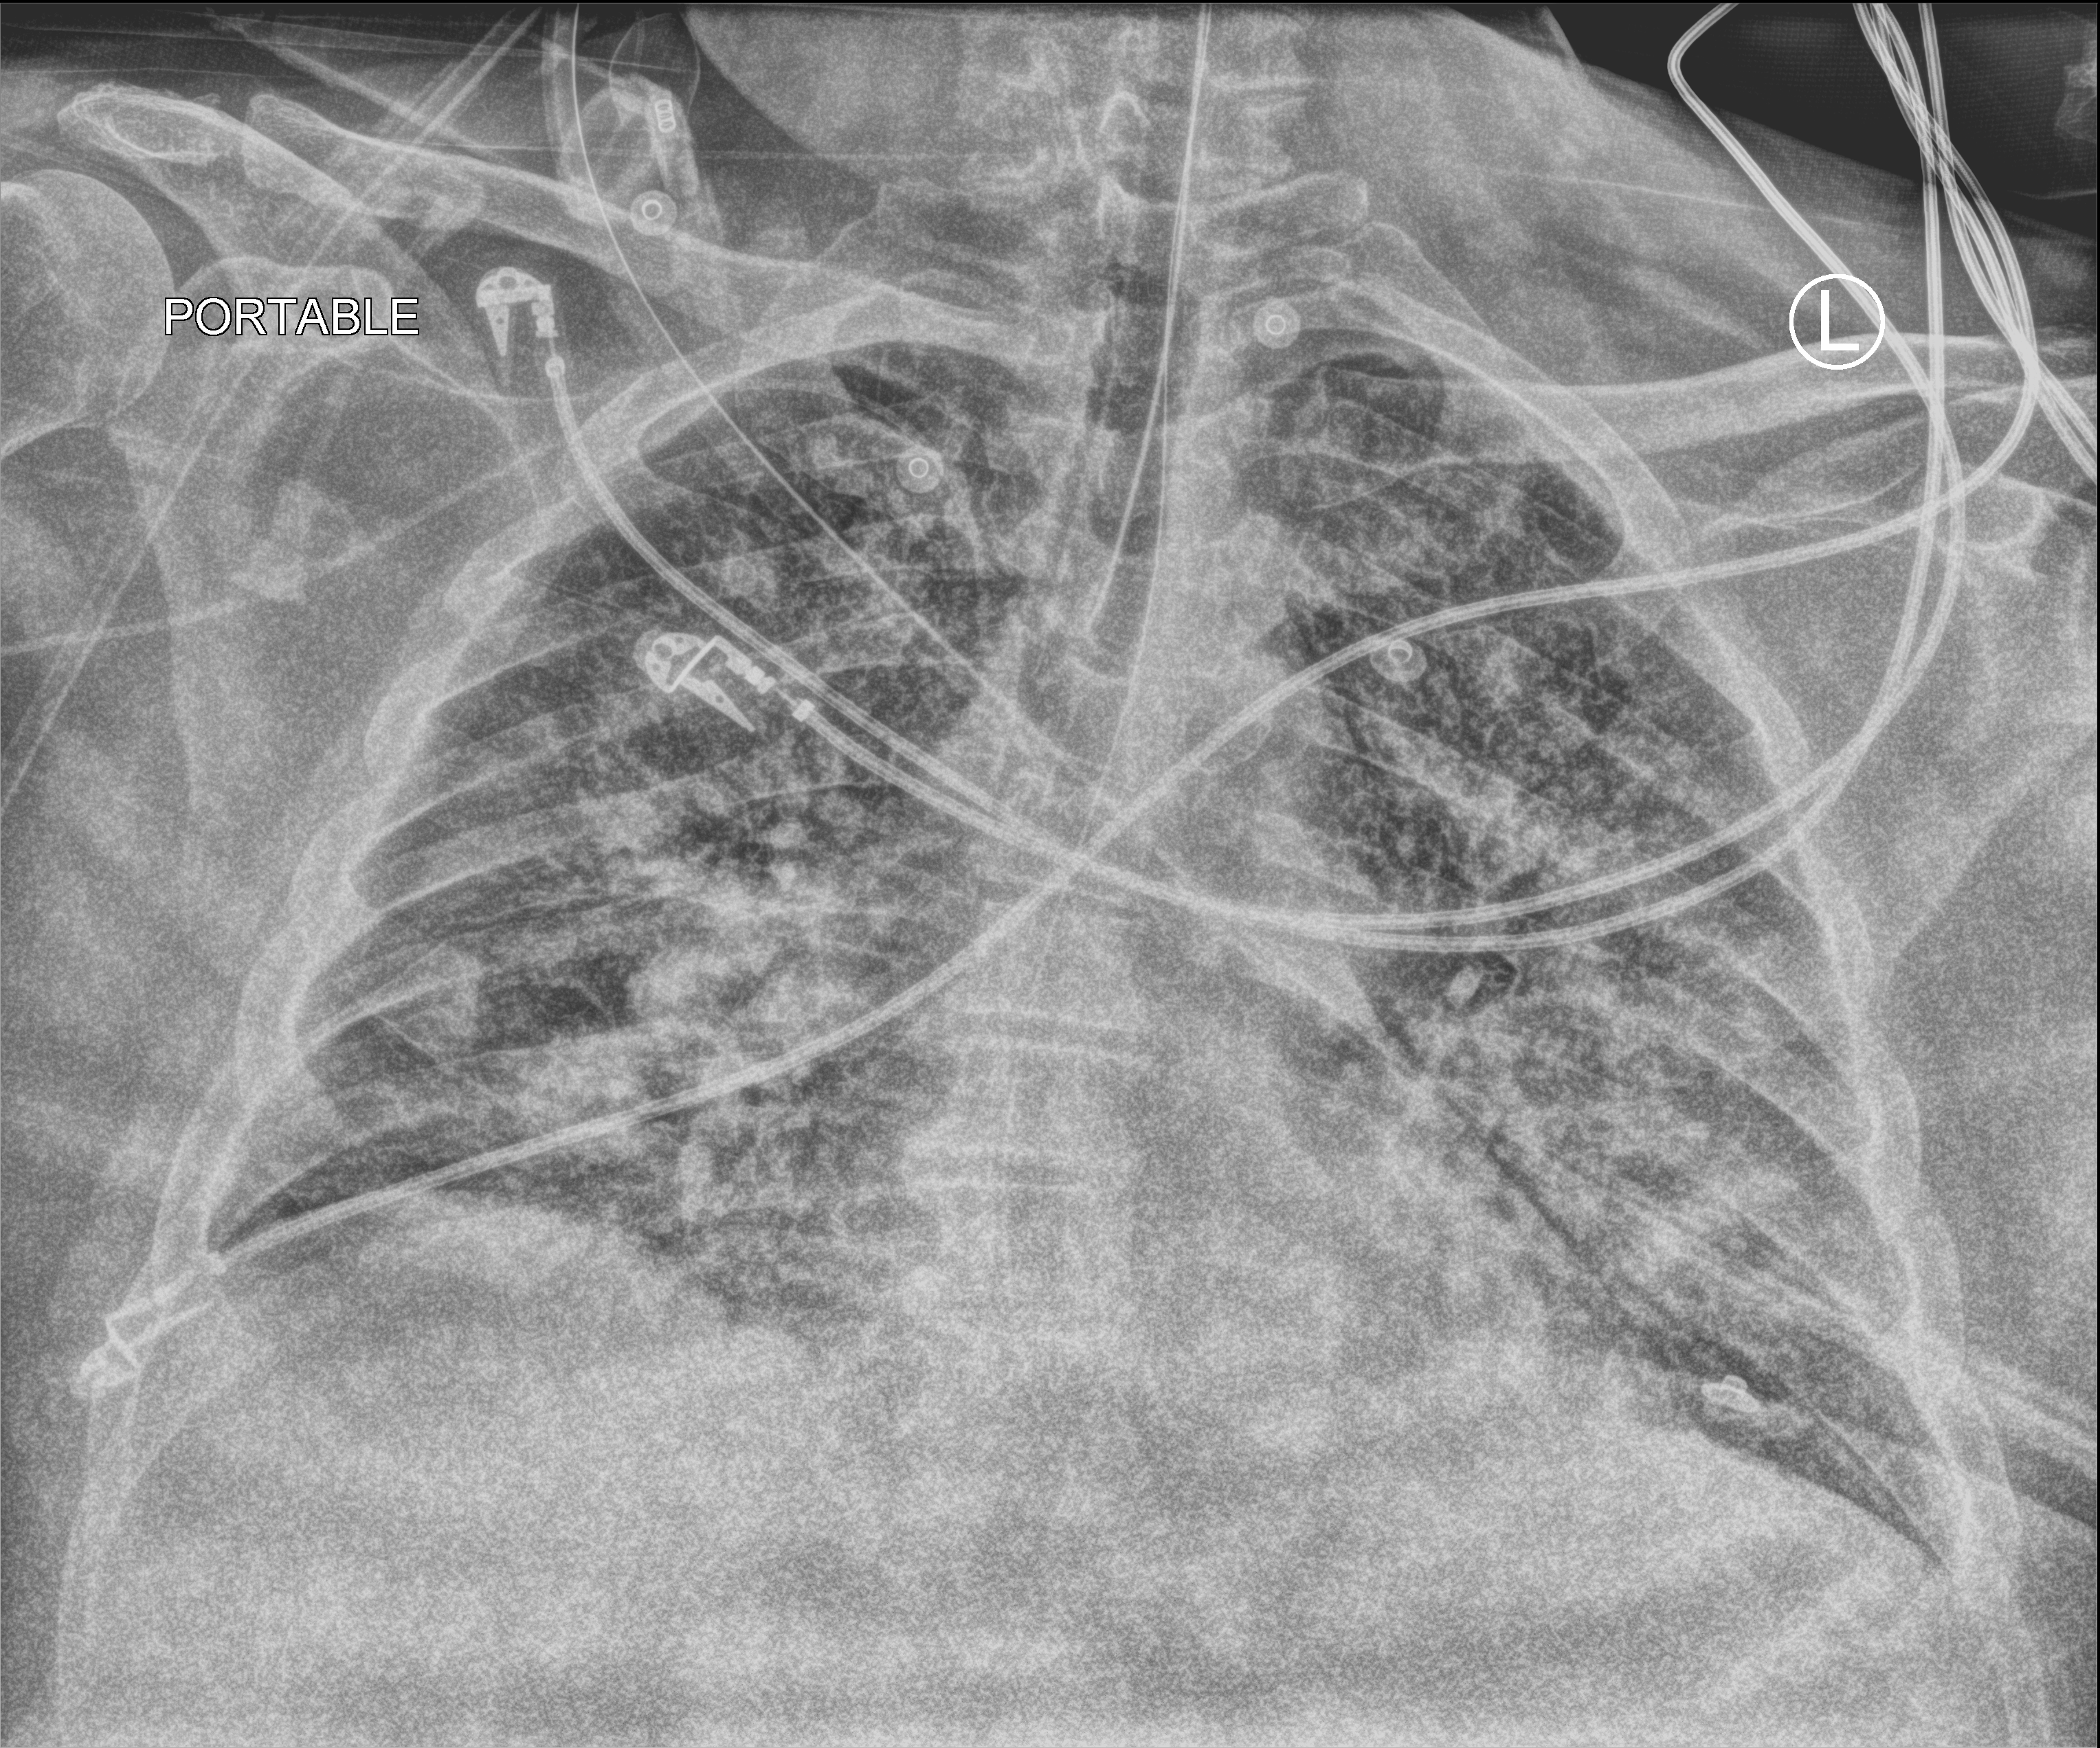
Portable chest radiograph; anteroposterior (AP) projection. Patient hospitalised with COVID-19; male, aged 60–74 years.
From the hospital-stay record, not from the radiograph (when in the stay this image was taken is not recorded): mechanically ventilated during this hospital stay: yes; length of hospital stay: 13 days; admitted to intensive care during this hospital stay: yes.